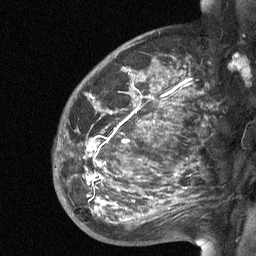
Breast MRI (dynamic contrast-enhanced), one sagittal slice. Slice 44 of 64 in the series (ordered by position). Dynamic contrast-enhanced study with each time point stored as its own series, time point 2 of 3 at this slice position (early post-contrast, ordered by acquisition time). 1.5 T. TE 4.8 ms, TR 27 ms. 2 mm slice thickness. 256 × 256 image matrix, field of view 200 × 200 mm. Patient: female, 50 years. From the clinical record (not read from this slice): setting: breast cancer imaged before/during neoadjuvant chemotherapy; receptor status: HER2-positive.
Outlined on this slice (semi-automatic segmentation, software-assisted and operator-edited):
- analysis volume of interest (the breast-tissue region the enhancement analysis was run in; not a lesion): bounding box (x1, y1, x2, y2) in pixels: (53, 91, 204, 227)
- tumour enhancement mask (voxels above the 90 % enhancement threshold inside the analysis volume of interest): (87, 139, 103, 203)